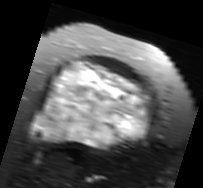
MRI of an extremity soft-tissue mass, one axial slice. Slice 52 of 91 in the series (ordered by position). T2-weighted fat-saturated. MR volume resampled by the dataset authors to the PET/CT grid (not the native acquisition matrix). 3.27 mm slice thickness. 203 × 188 image matrix, field of view 198 × 184 mm. Female patient. Case-level facts recorded for this patient, not image findings: histological type: malignant solitary fibrous tumor; grade: intermediate; site of the primary tumour: right thigh.
Structures marked on this image (expert contour drawn on MRI and transferred to this co-registered scan by the dataset authors):
- gross tumour volume including surrounding oedema: box from (x=31, y=60) to (x=155, y=150) px
- gross tumour volume (mass): (x=31, y=62)–(x=150, y=148)